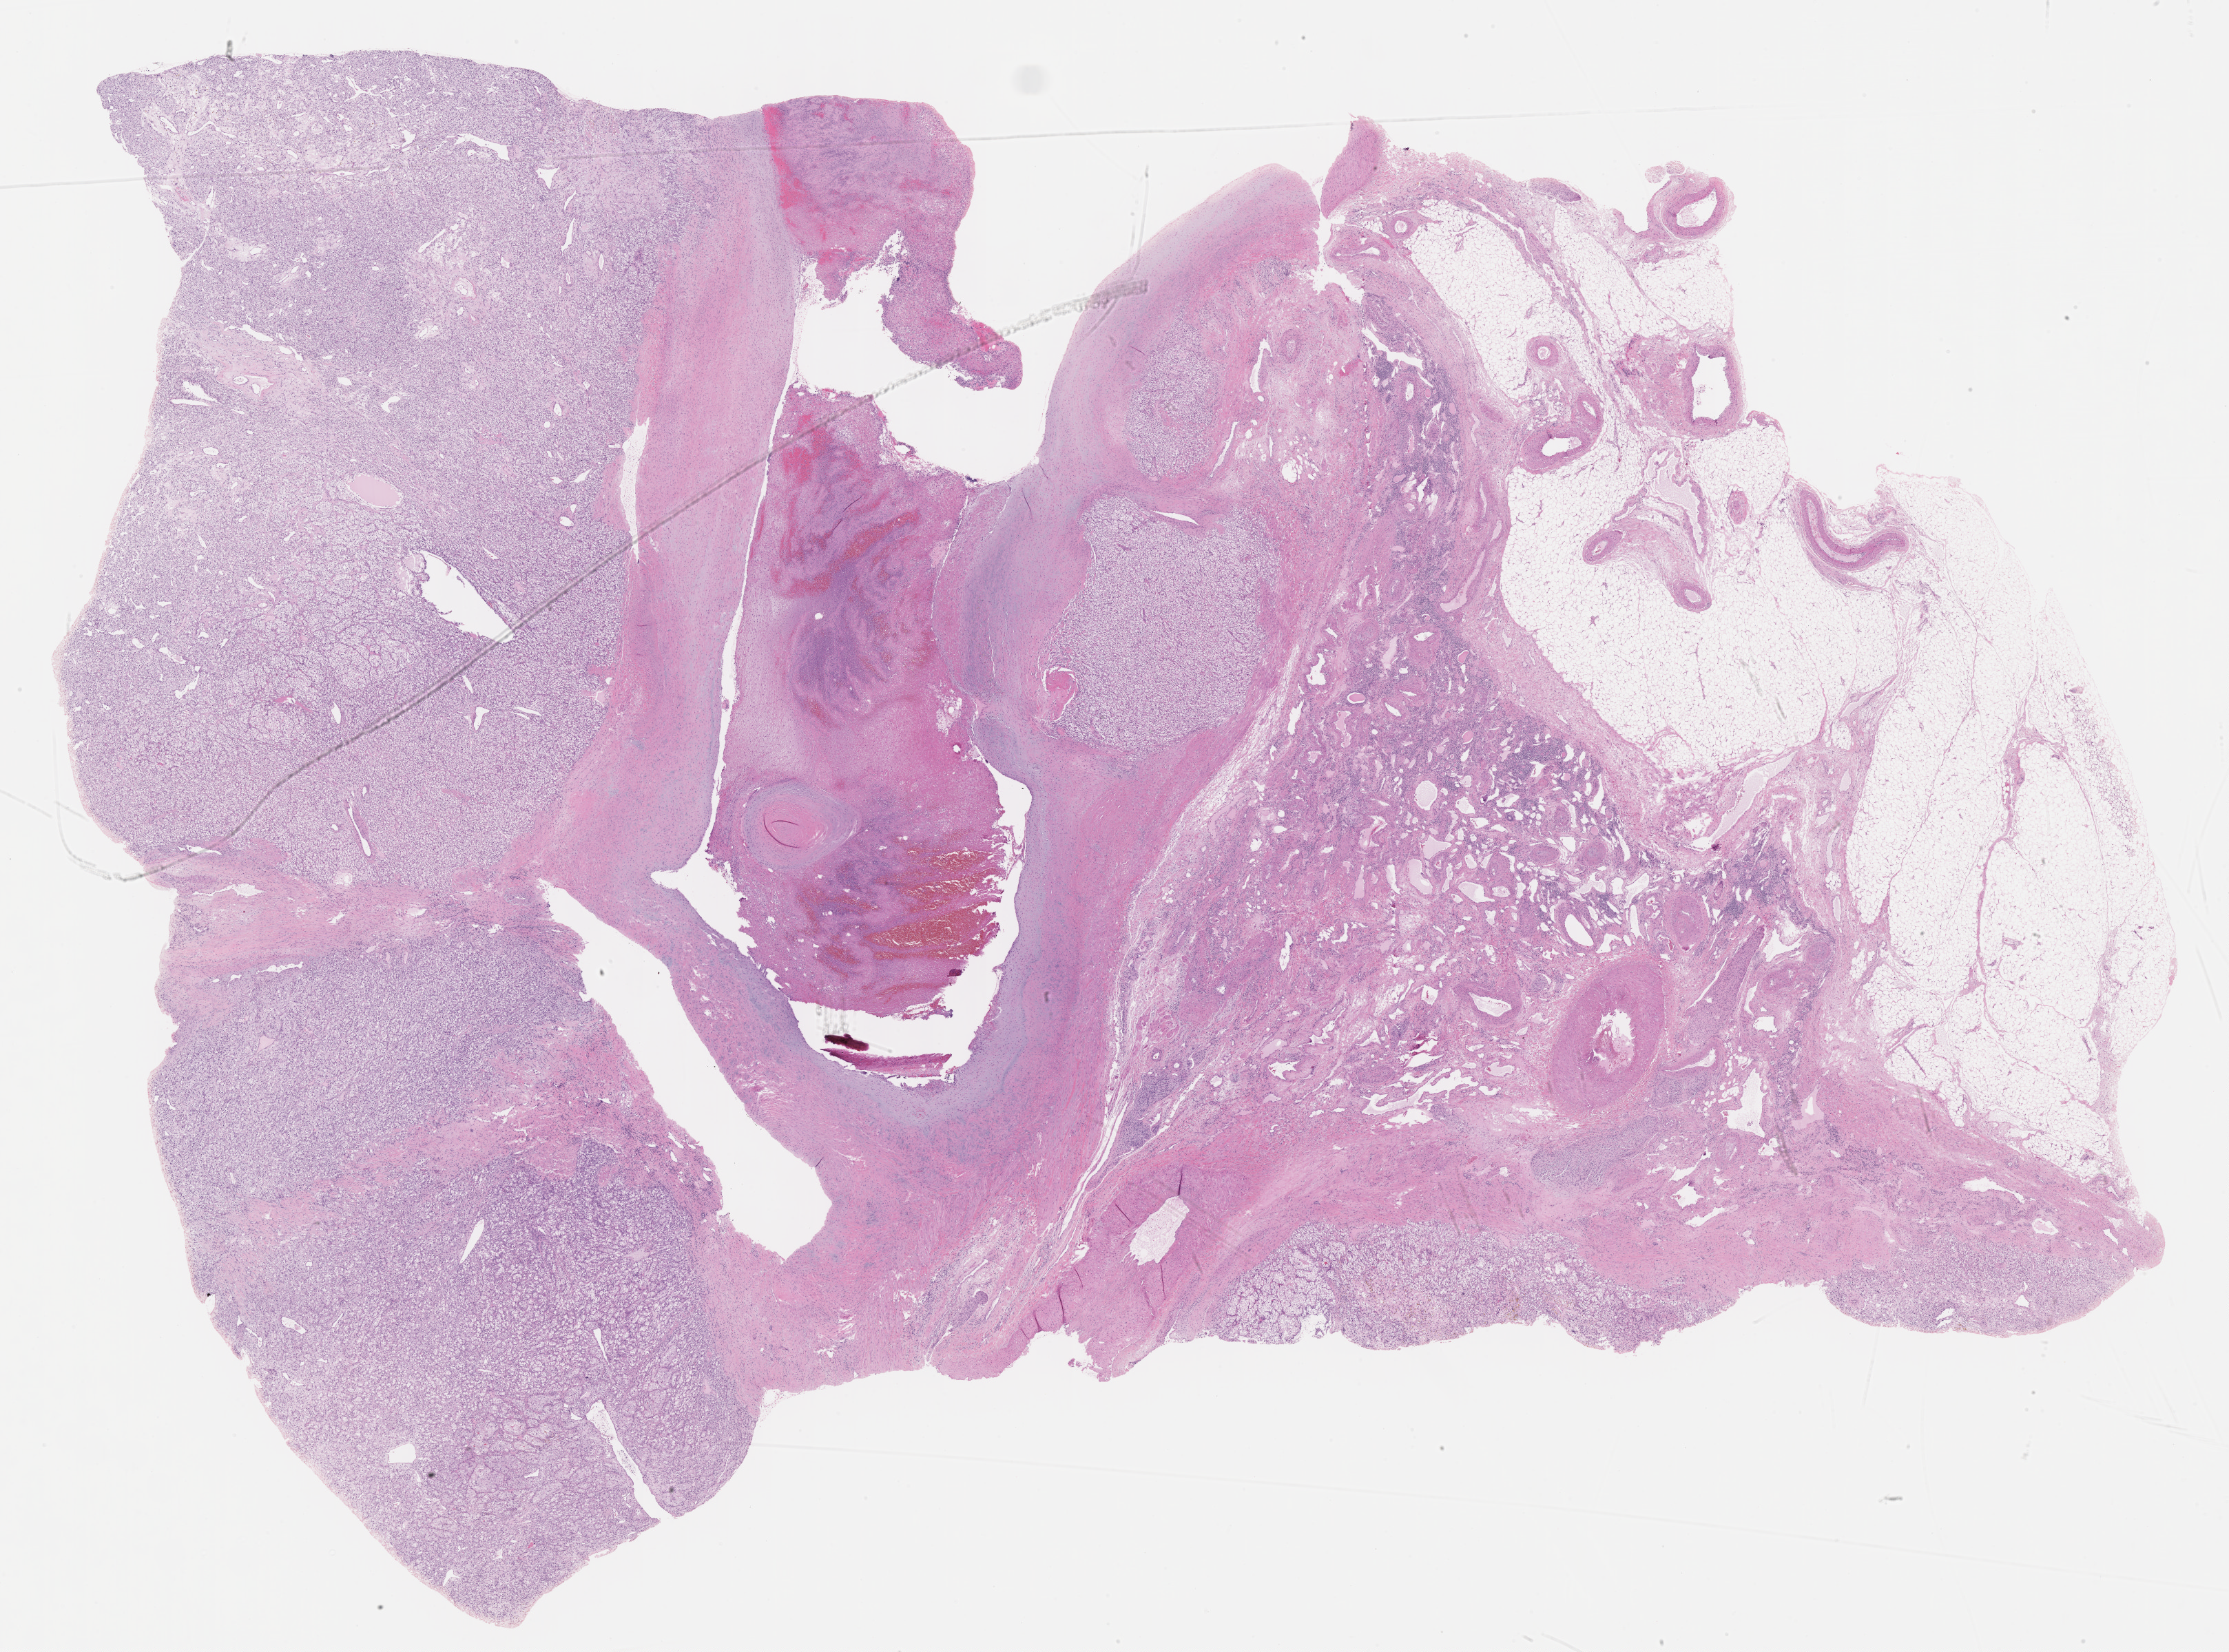
Hematoxylin and eosin (H&E) stained whole-slide image — low-resolution overview of the scanned area, about 26.2 x 19.4 mm; formalin-fixed paraffin-embedded (FFPE) diagnostic section; kidney, primary tumour sample. Female, age 48 years at initial diagnosis.
Pathologic diagnosis: Clear cell adenocarcinoma, NOS.